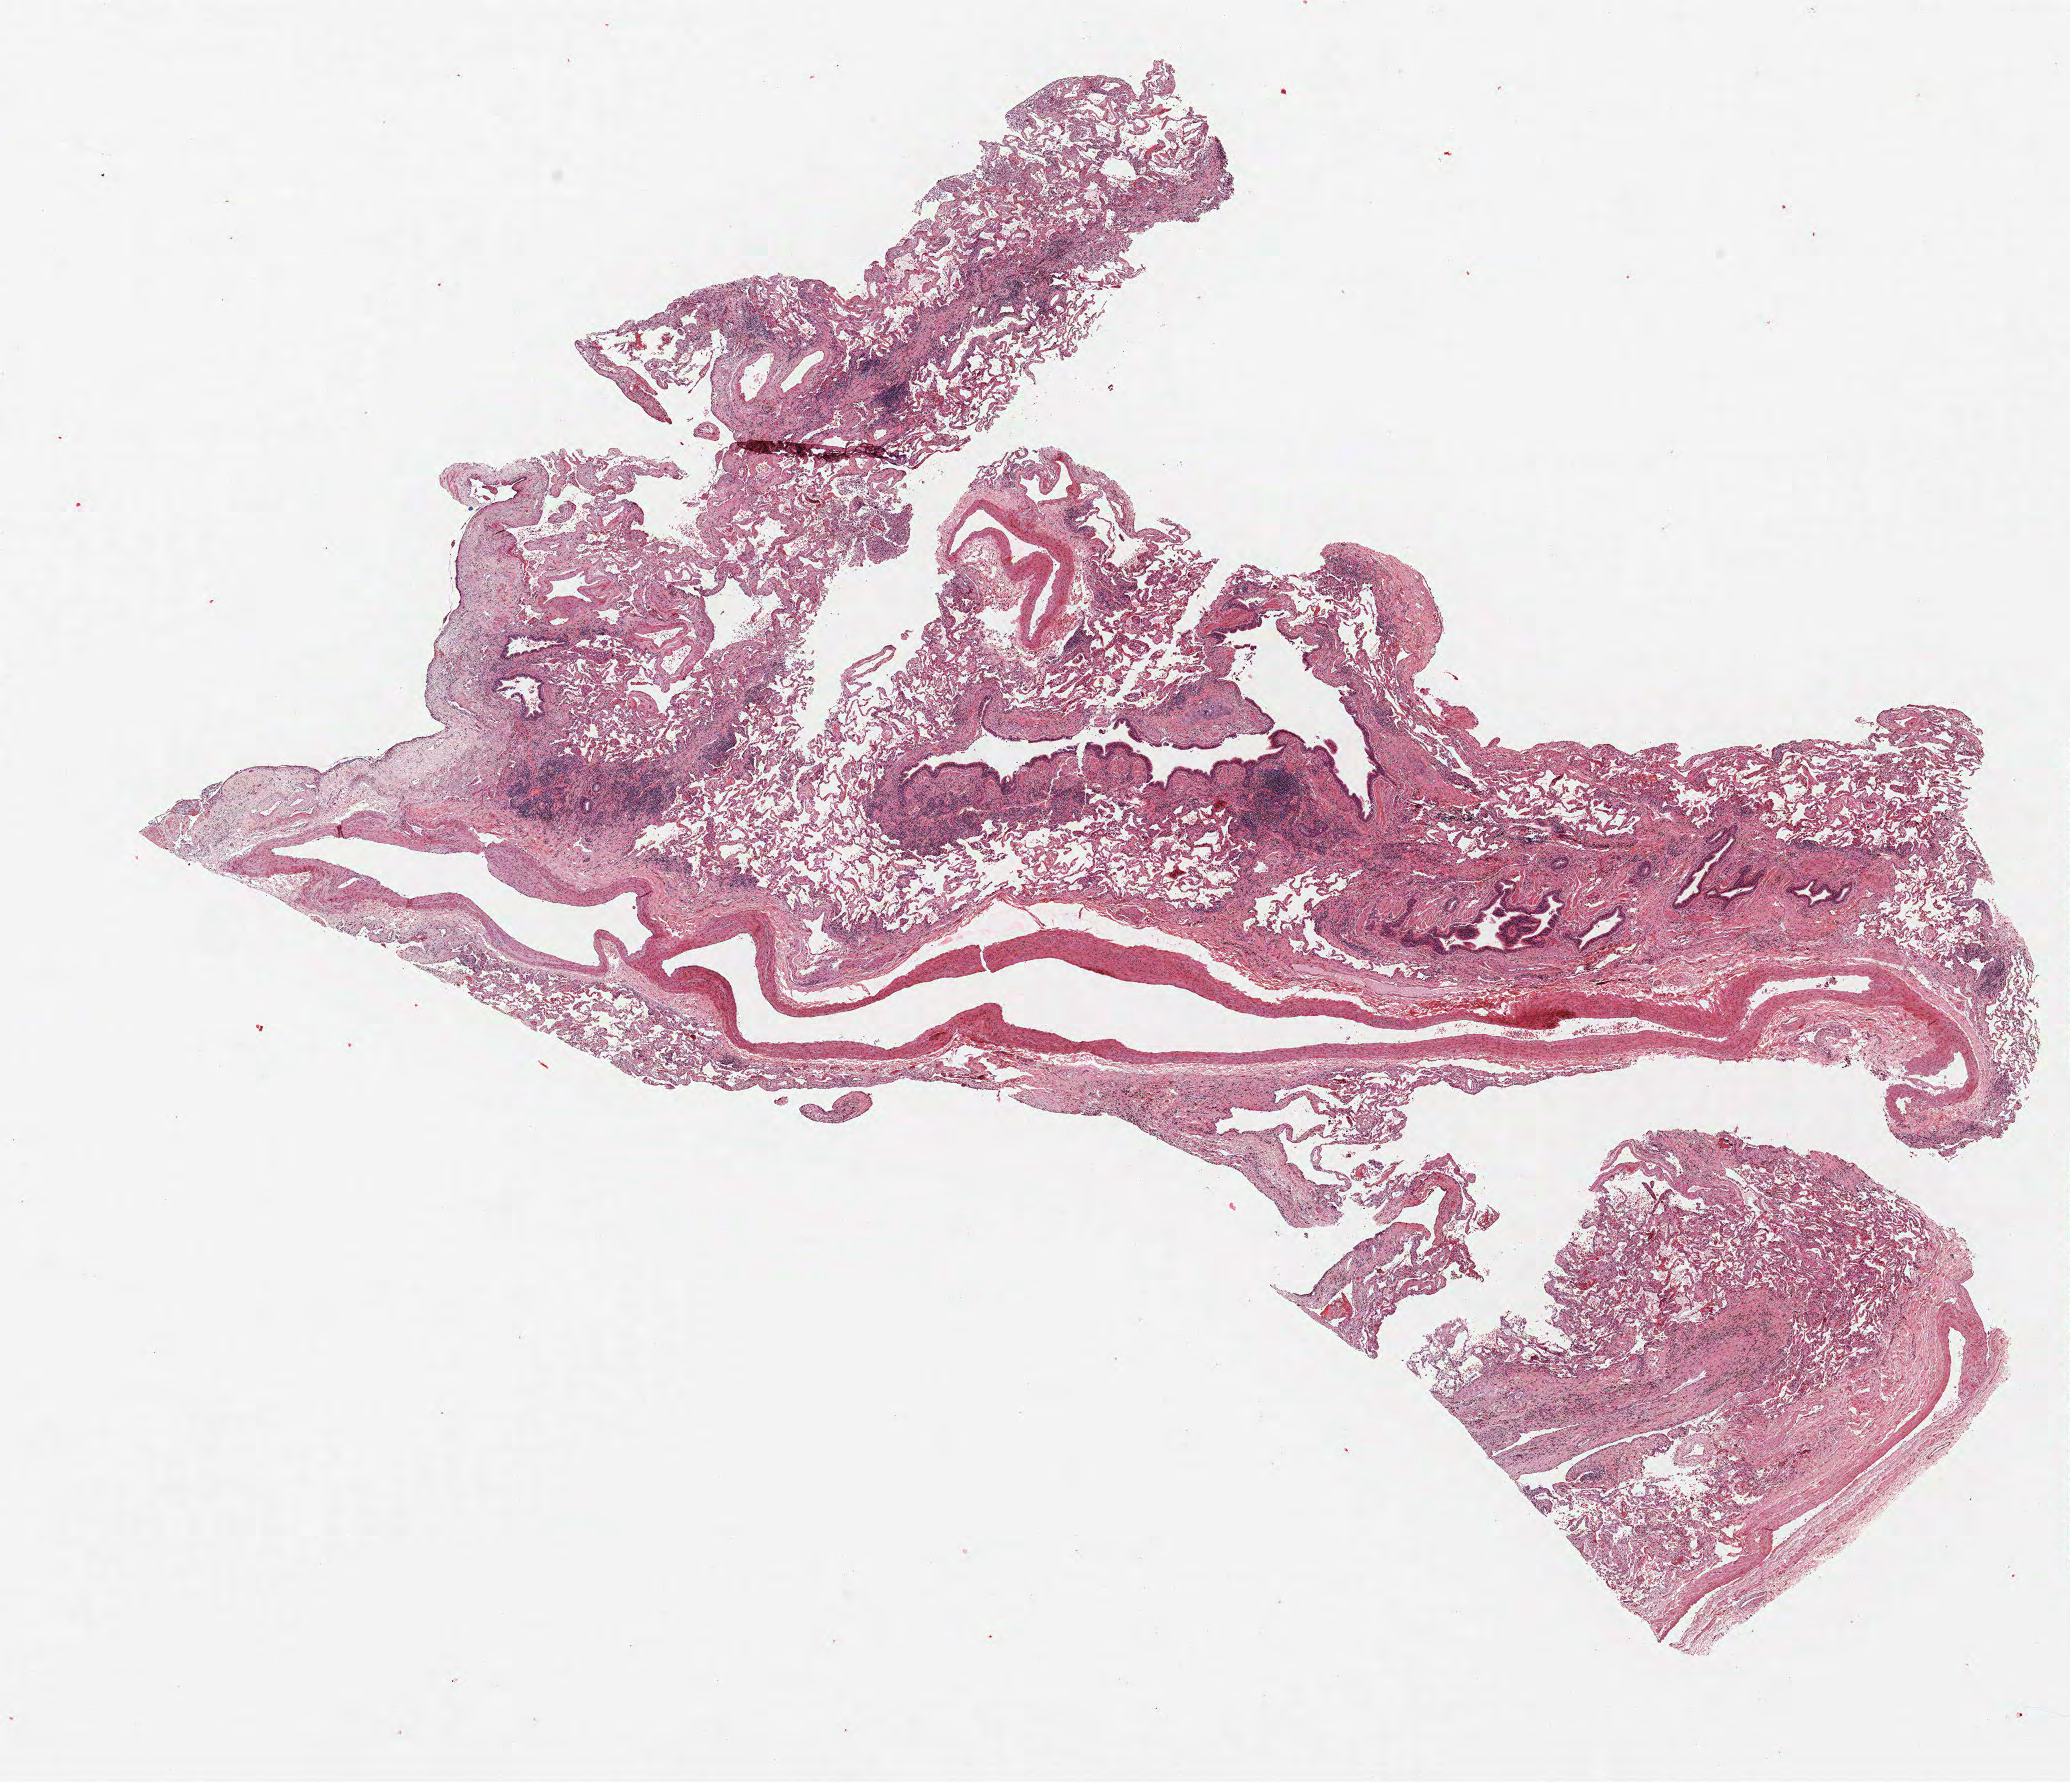
H&E-stained whole-slide image — whole scanned area (about 16.6 x 14.3 mm, slide scanned at 40x) shown as a low-resolution overview. Formalin-fixed paraffin-embedded (FFPE) section. Lung tissue. Male patient, aged 63 at enrolment. Former smoker at enrolment. Grade: moderately differentiated (G2).
Primary tumour location (clinical record): right upper lobe. Tumour size (pathology): 80 mm. Participant's lung-cancer diagnosis: Squamous cell carcinoma, NOS (ICD-O-3 8070/3). Stage (AJCC 6th edition): IB.